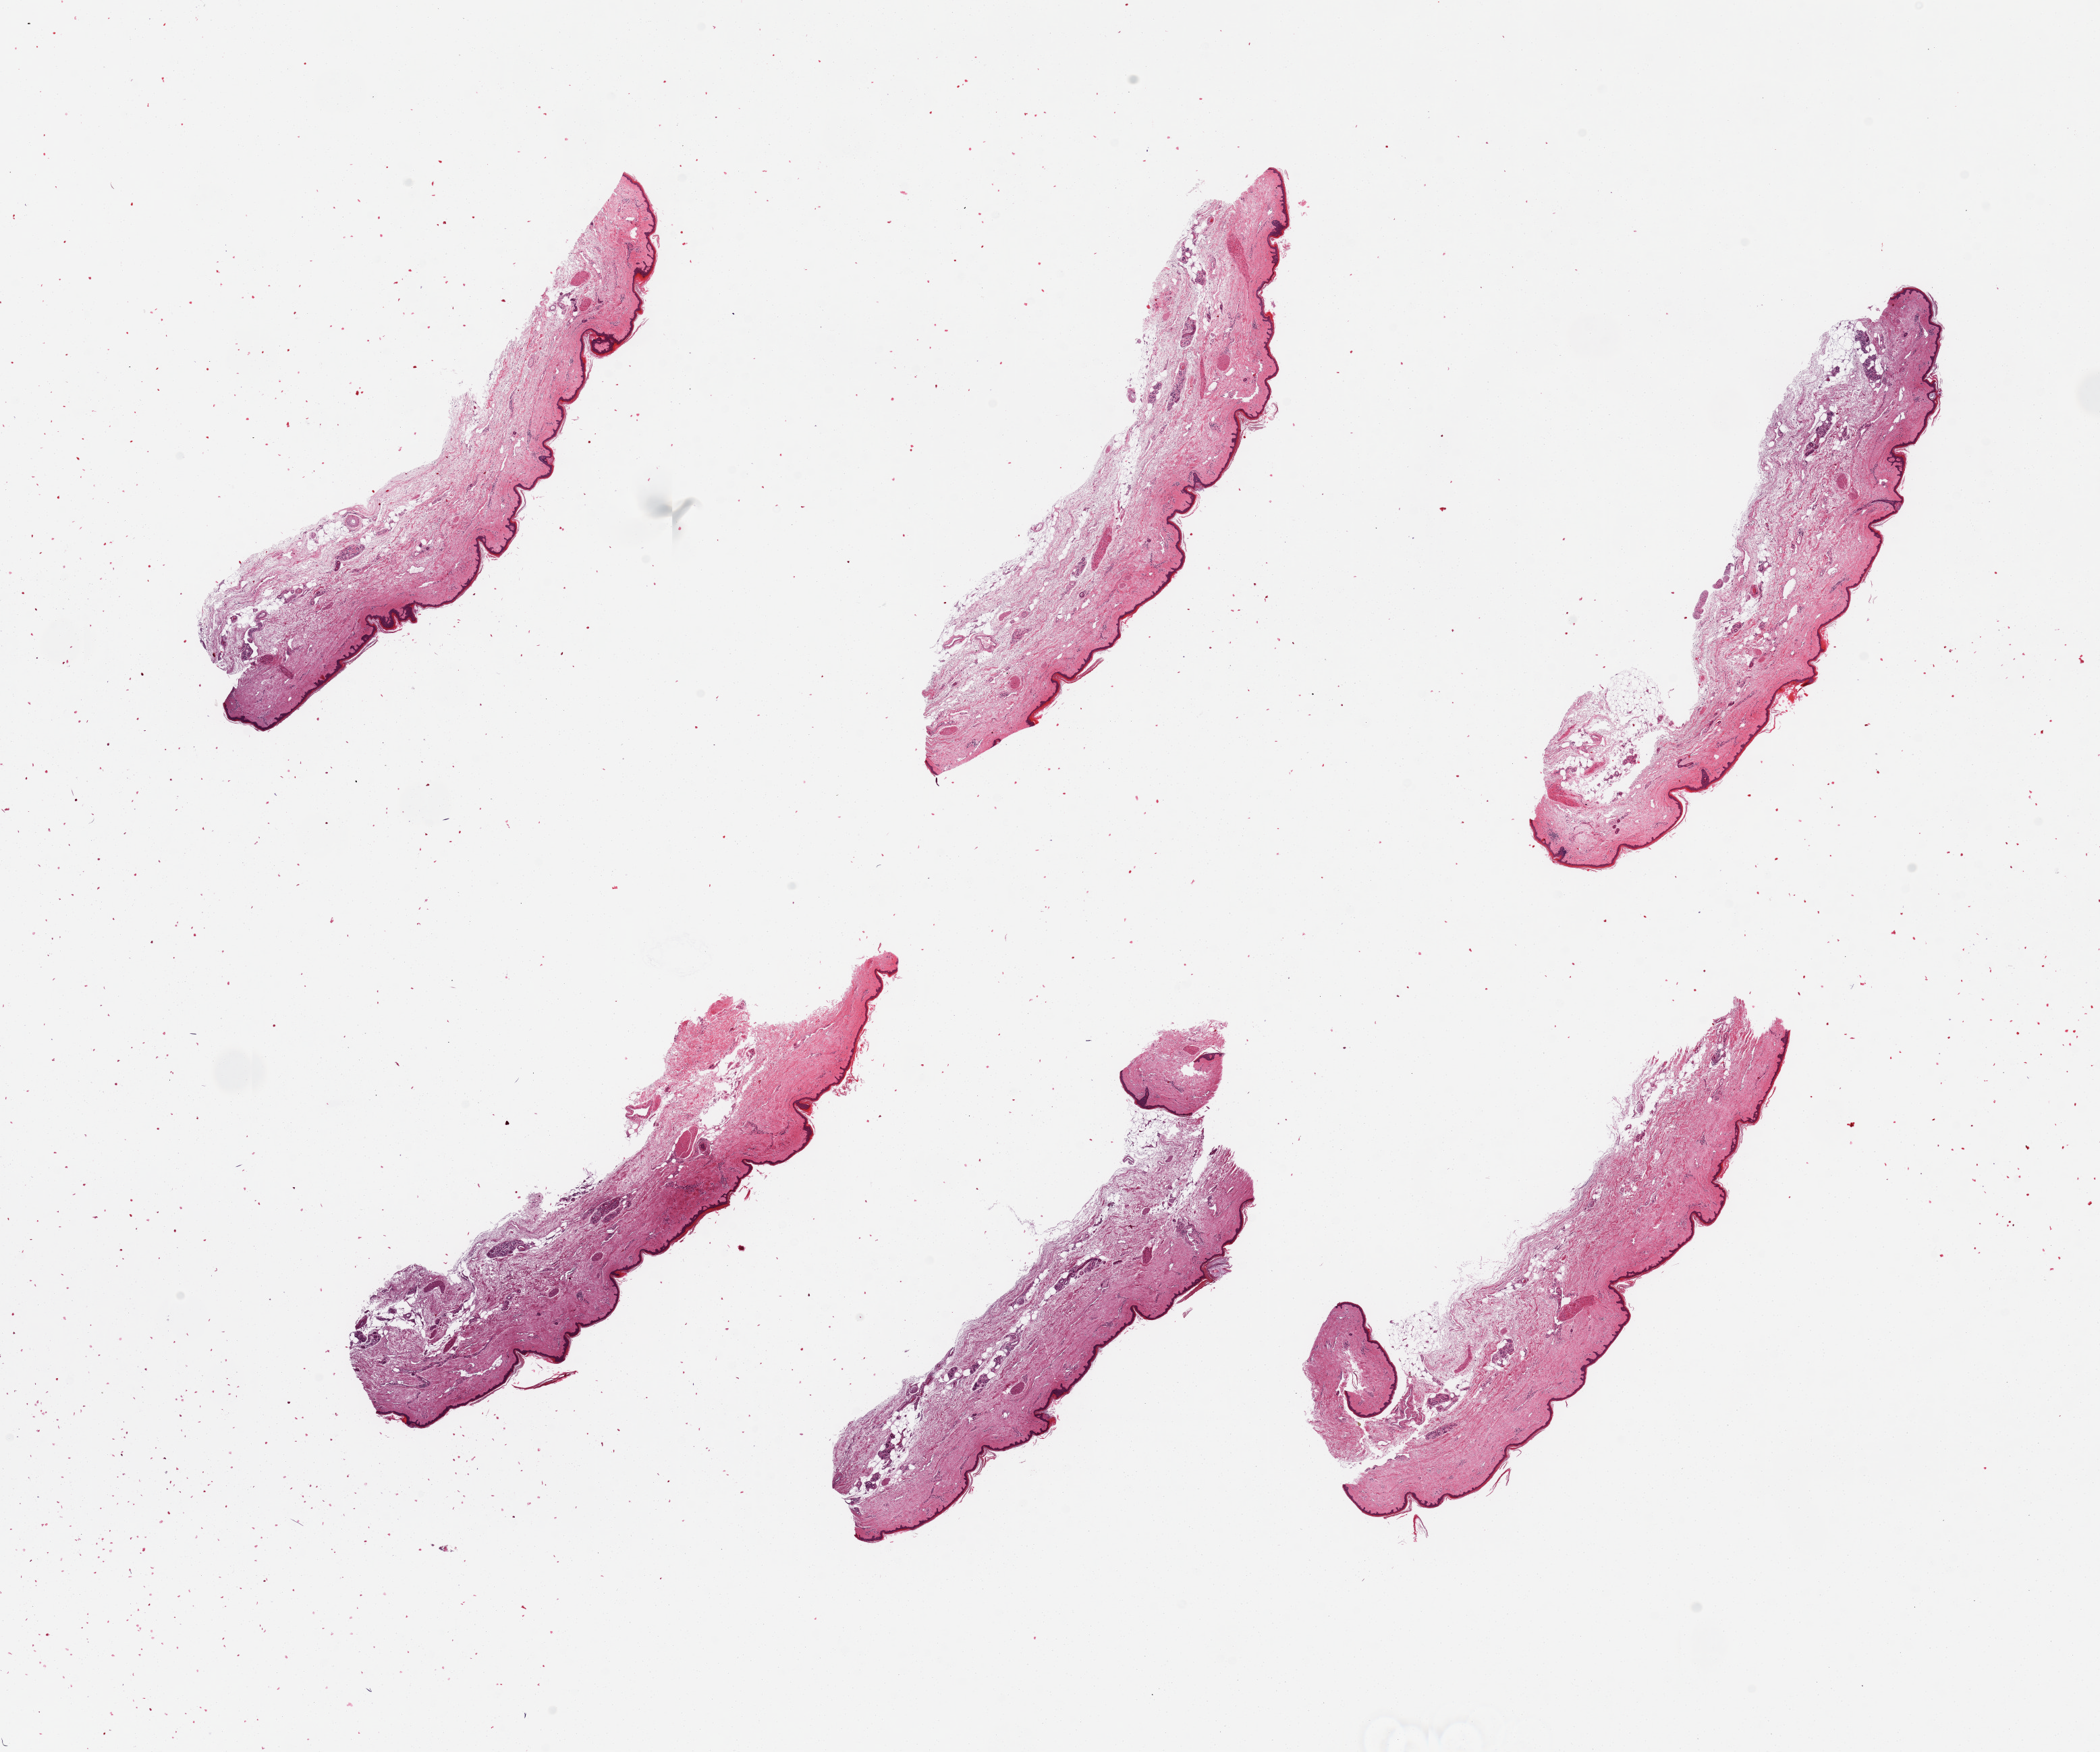
Digitized hematoxylin and eosin (H&E)-stained section, shown as a low-resolution overview of the whole scanned area (about 24.6 x 20.5 mm, from a 20x scan). PAXgene-fixed paraffin-embedded (PFPE) section. Target tissue: skin of lower leg. Tissue donor sample.
Review note (as recorded): 6 pieces; sweat glands moderately autolyzed.